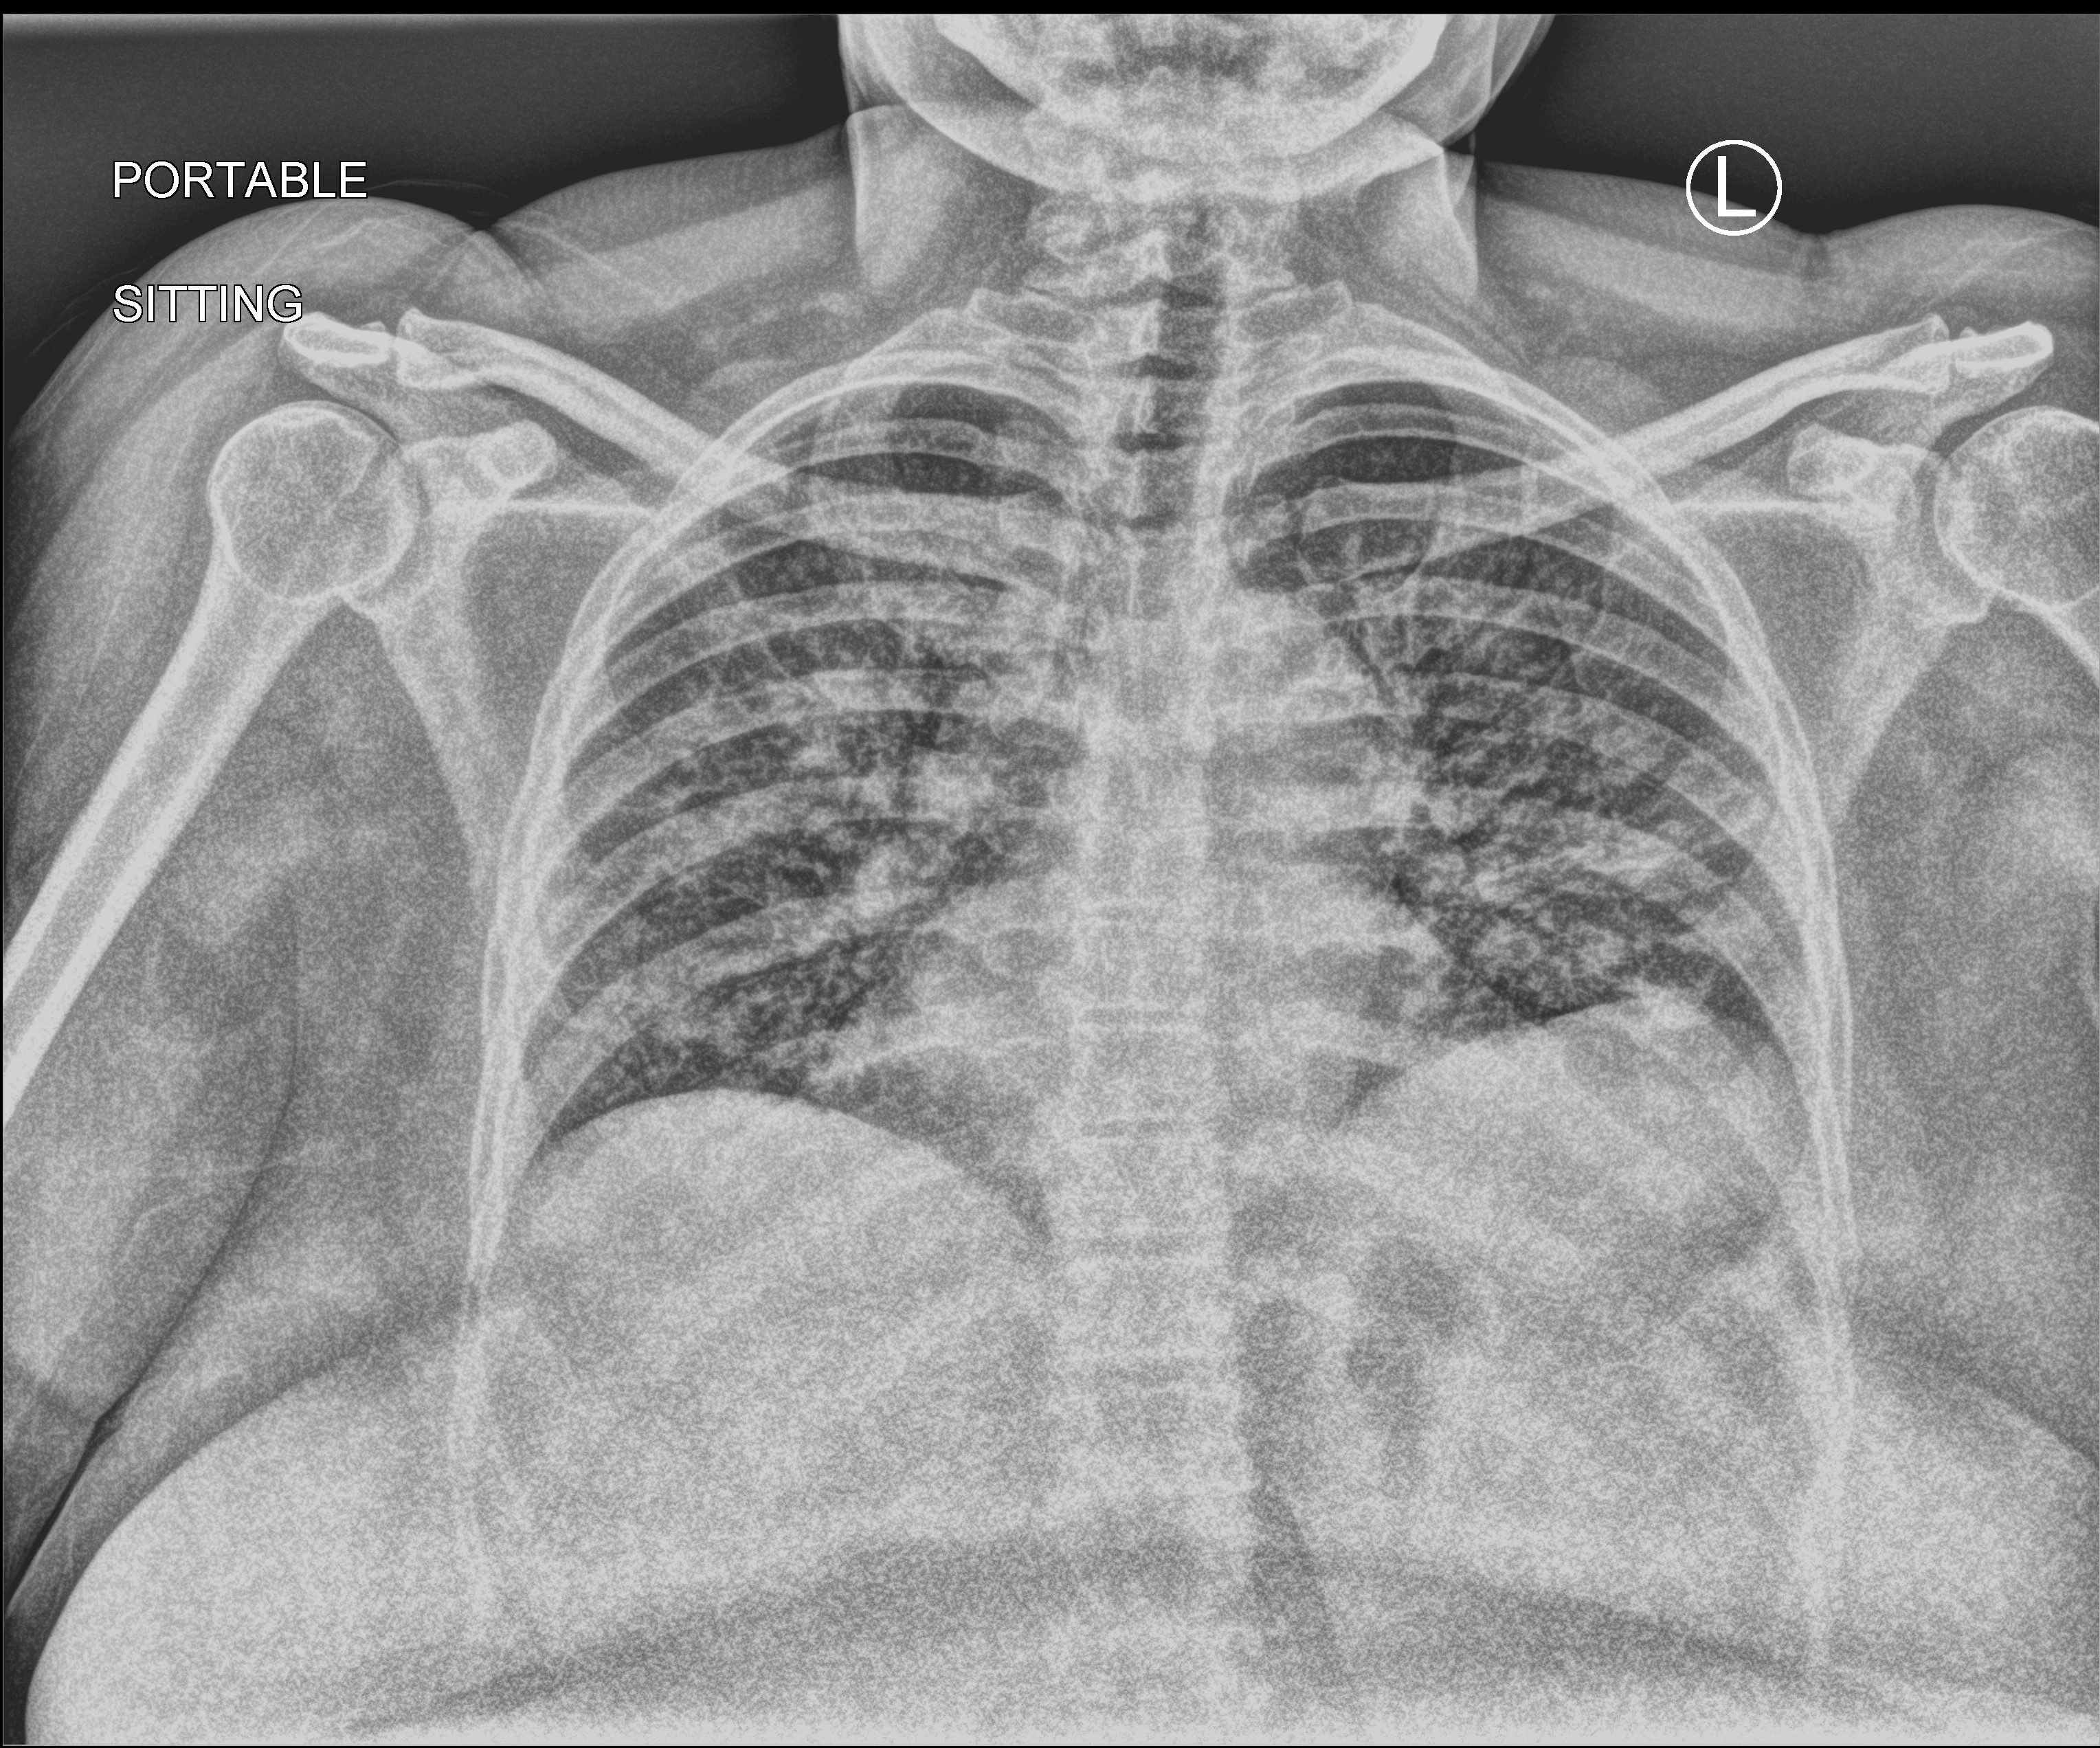
Bedside chest radiograph (computed radiography), anteroposterior (AP) projection. Patient hospitalised with COVID-19; female, aged 60–74 years.
From the hospital-stay record, not from the radiograph (when in the stay this image was taken is not recorded):
- mechanically ventilated during this hospital stay: no